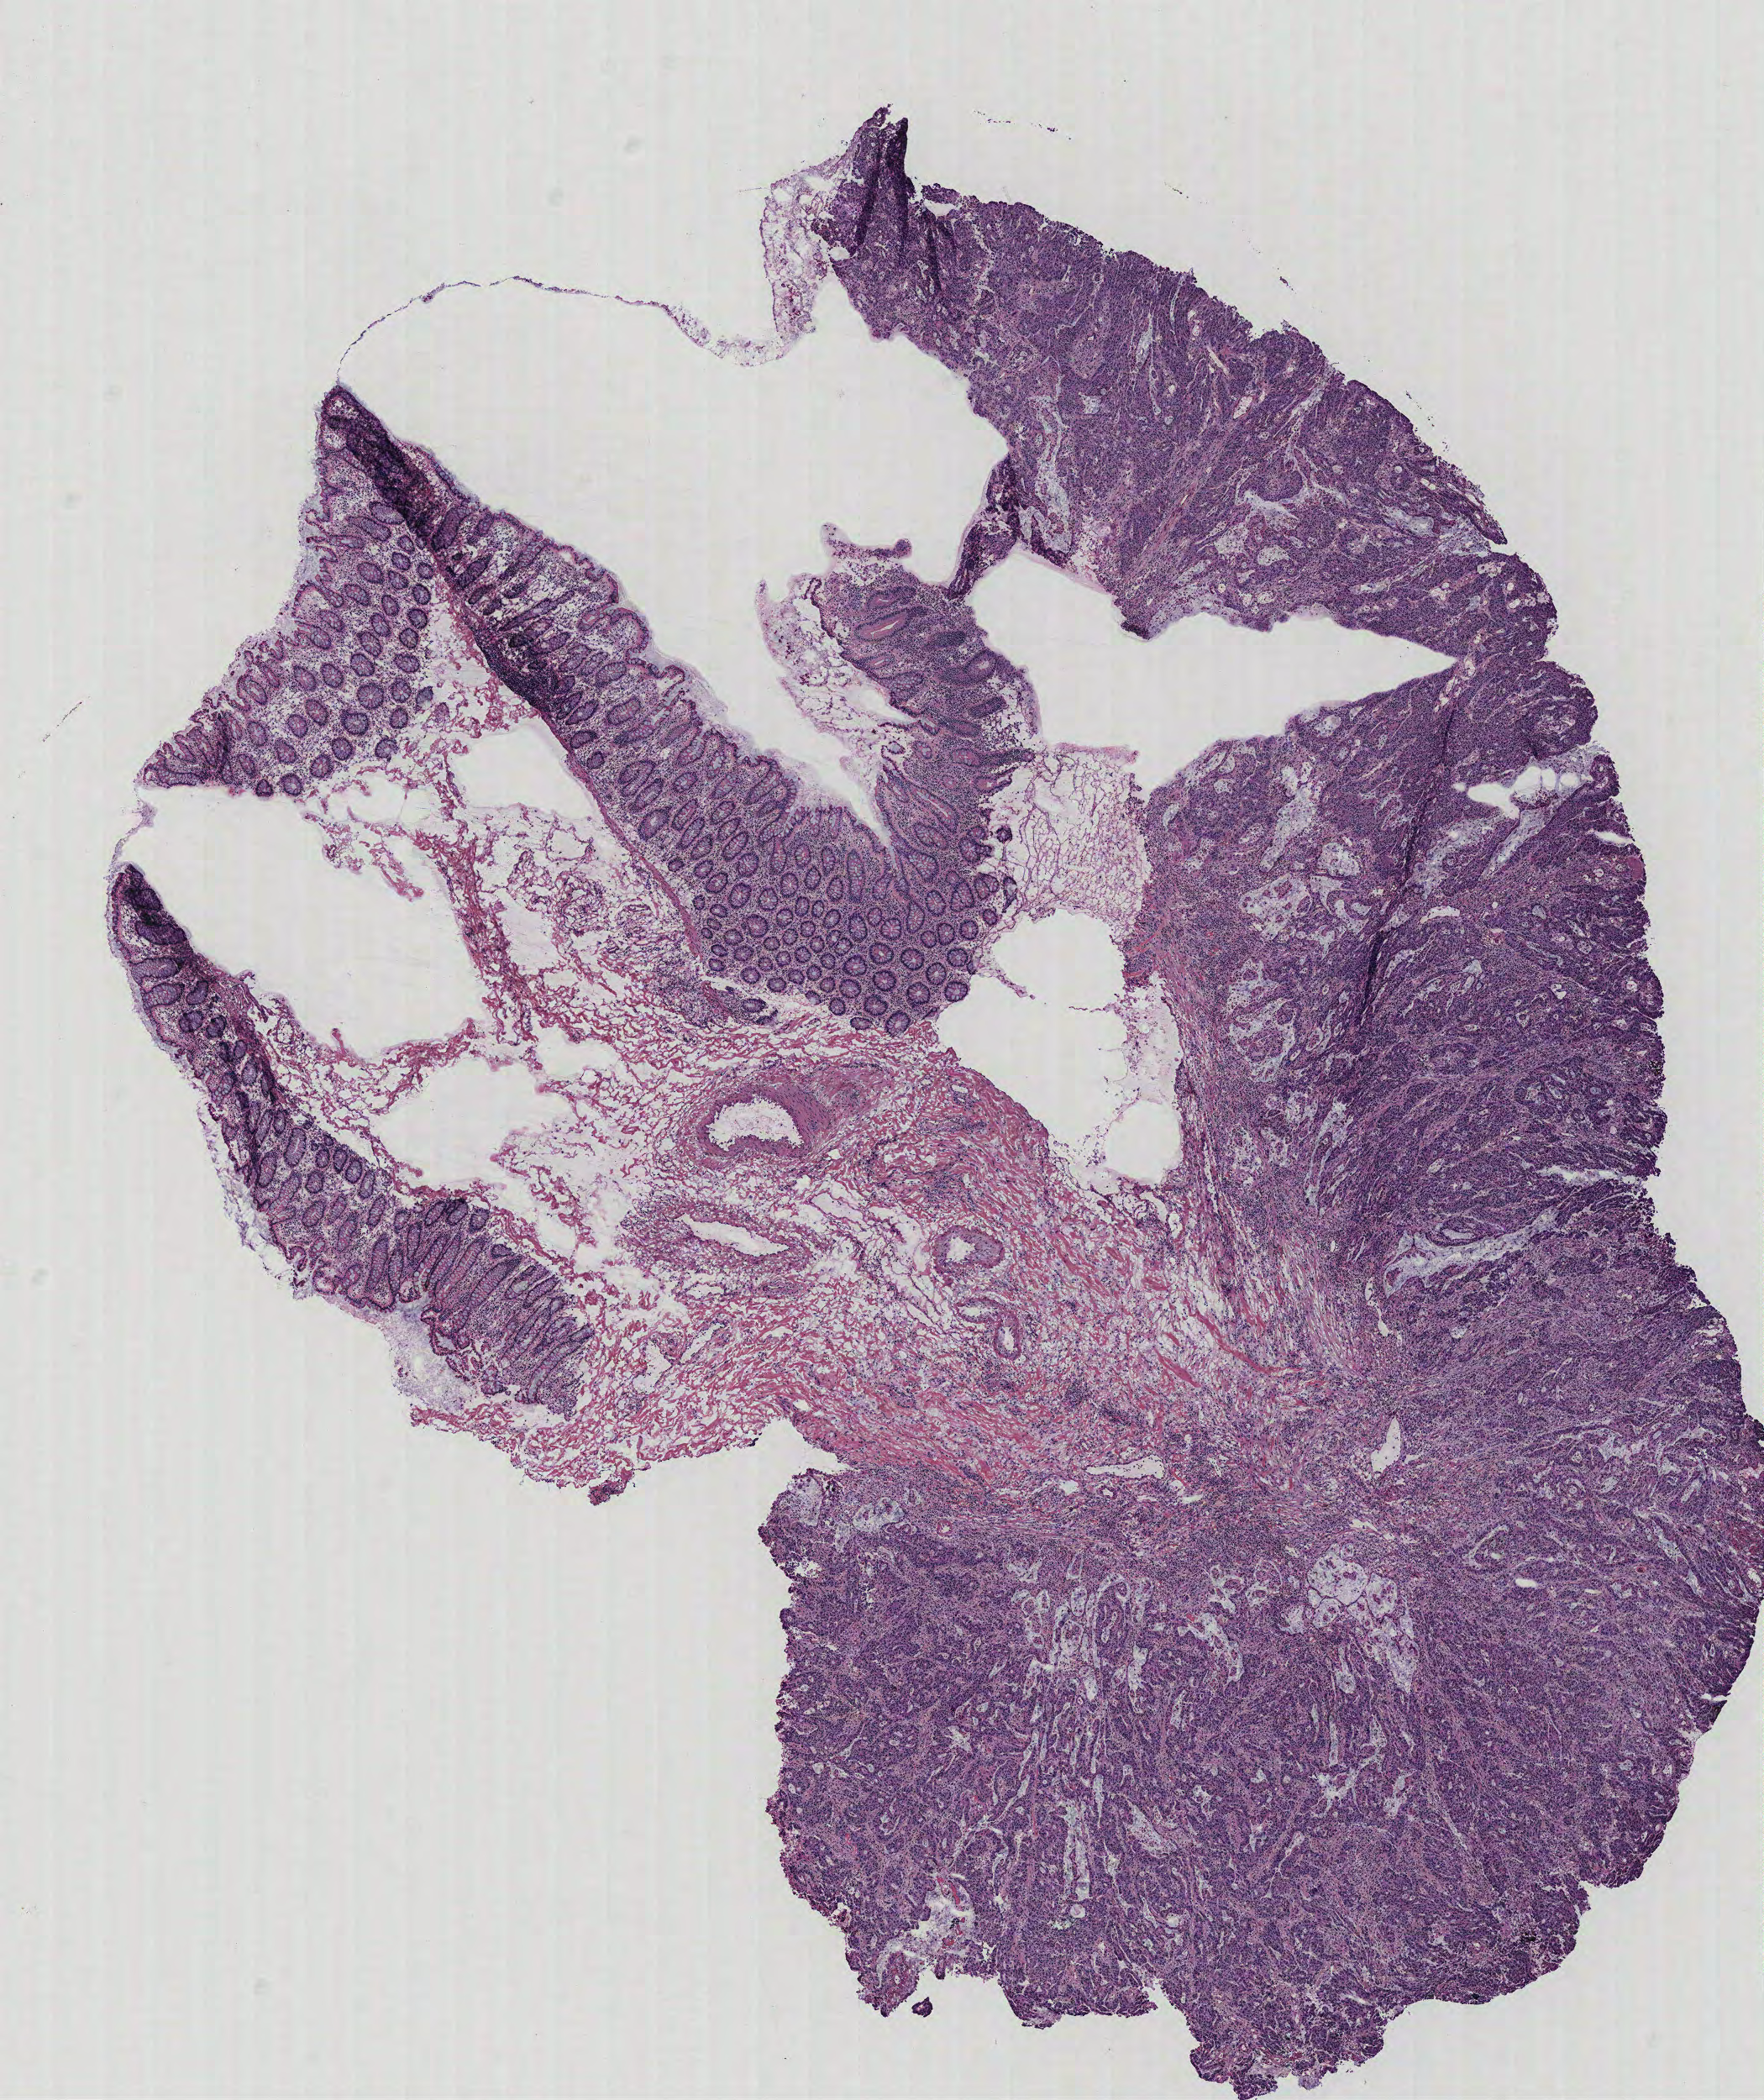
Whole-slide histology image, H&E-stained — shown as a low-resolution overview of the whole scanned area (about 8.4 x 10.0 mm, slide scanned at 40x), colon, tissue type not recorded.
• patient diagnosis (cohort enrolment): colon cancer (colon)